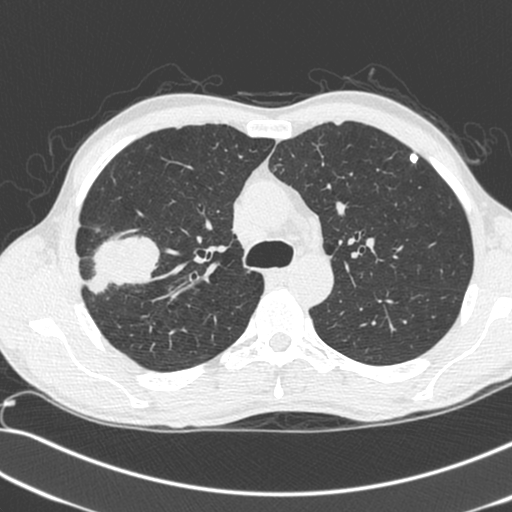
Chest CT (low-dose screening protocol), one axial image; baseline screening round; lung window (W 1500 / L -600 HU); standard (soft-tissue) reconstruction kernel (C); slice 77 of 281 in the series; 512 × 512 image matrix. Male participant, aged 55 years at enrolment. Current smoker at enrolment.
Lesion marked by an expert reader, bounding box <71,232,152,305> (left, top, right, bottom; pixels). Reader record for this screening exam (exam-level; its link to the box is not recorded): non-calcified nodule or mass ≥4 mm, right upper lobe, 52 × 39 mm, spiculated (stellate) margins, soft tissue attenuation. Official screen result: positive, change unspecified: nodule(s) >= 4 mm or enlarging nodule(s), mass(es), or other non-specific abnormalities suspicious for lung cancer. Later outcome: lung cancer diagnosed 25 days after this screen — large cell neuroendocrine carcinoma, right upper lobe, poorly differentiated (G3), stage IIB (AJCC 6th edition), 49 mm at pathology.